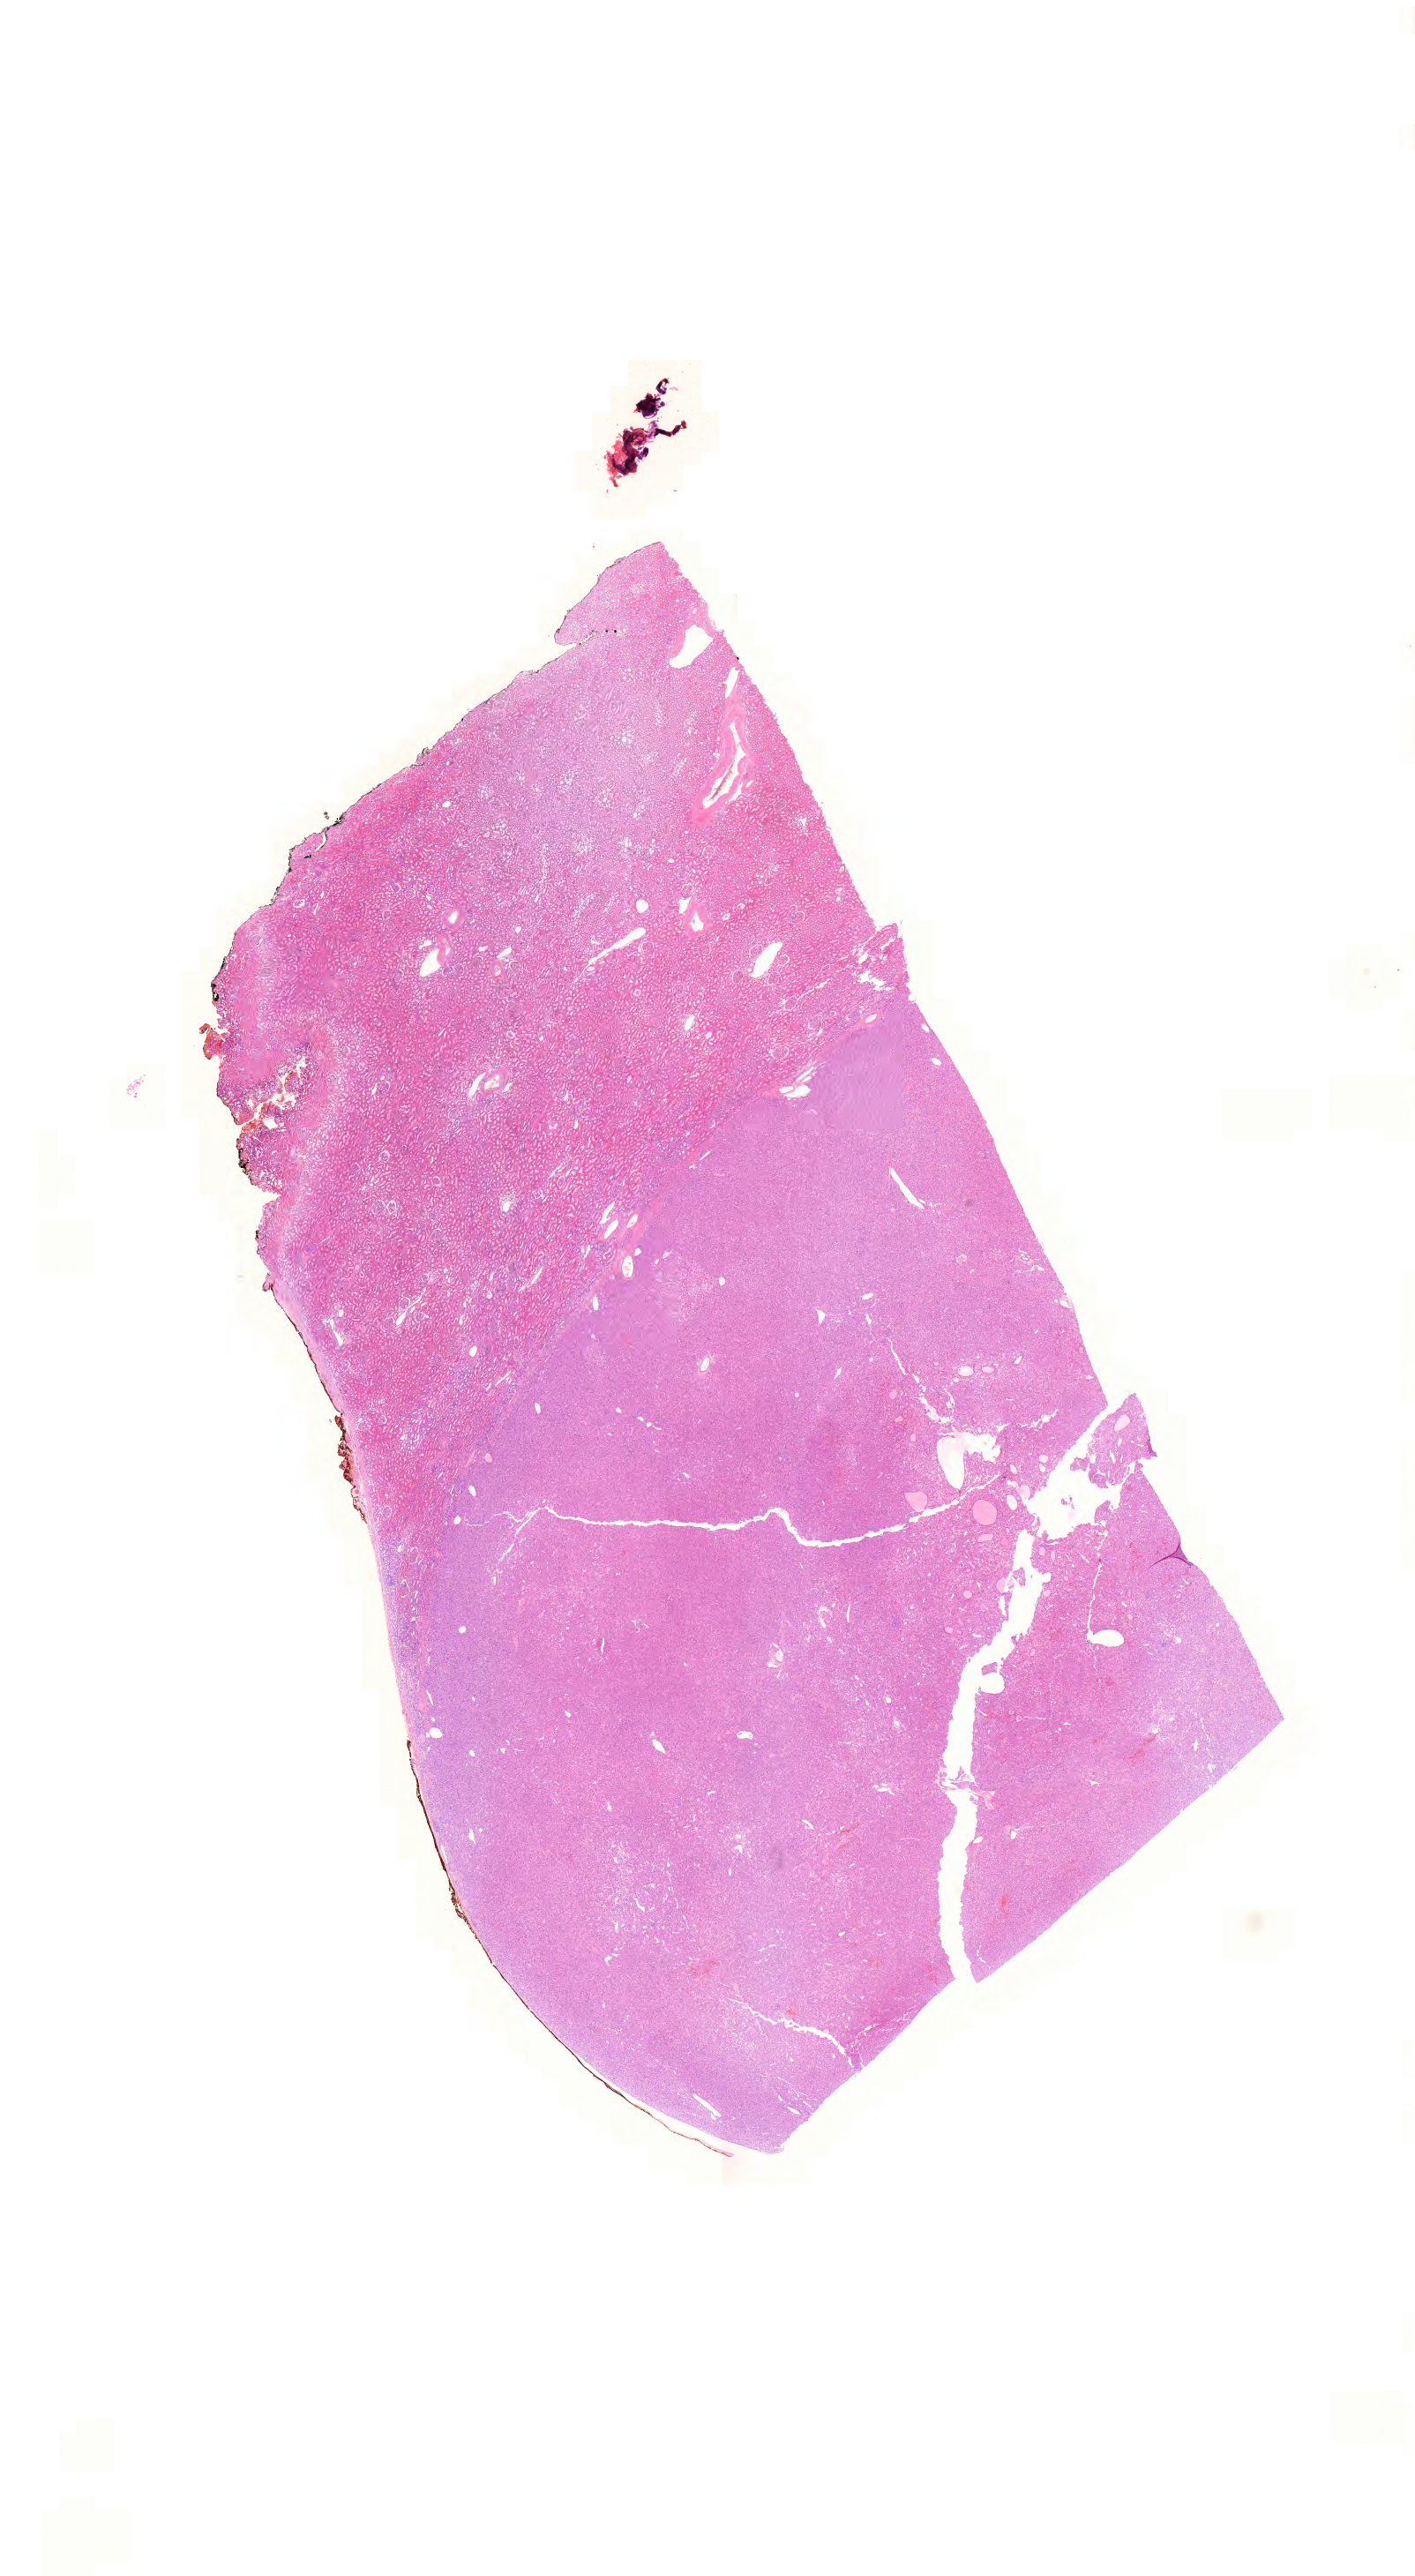
Whole-slide histology image, Hematoxylin and eosin (H&E) stained — a low-resolution overview of the entire scanned area, about 23.9 x 43.4 mm (acquisition: 20x scan); formalin-fixed paraffin-embedded (FFPE) diagnostic section; kidney, primary tumour sample. Female, age 47 years at initial diagnosis. Histologic grade: G1 (well differentiated).
AJCC pathologic stage: I (7th edition). Diagnosis: Clear cell adenocarcinoma, NOS.